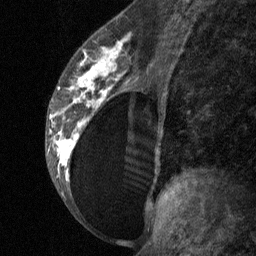
Breast MRI (dynamic contrast-enhanced), one sagittal slice; position 36 of 64 along the scan axis; dynamic contrast-enhanced study with each time point stored as its own series, time point 2 of 3 at this slice position (early post-contrast, ordered by acquisition time); 1.5 T; TE 4.8 ms, TR 27 ms; 2 mm slice thickness; 256 × 256 image matrix, field of view 180 × 180 mm. Patient: female, 34 years. Case-level facts recorded for this patient, not image findings: setting: breast cancer imaged before/during neoadjuvant chemotherapy; receptor status: HR-positive, HER2-negative.
Structures marked on this image (semi-automatically segmented with operator editing):
- analysis volume of interest (the breast-tissue region the enhancement analysis was run in; not a lesion): bounding box [x1, y1, x2, y2] px = [45, 23, 157, 197]
- tumour enhancement mask (voxels above the 90 % enhancement threshold inside the analysis volume of interest): [50, 39, 125, 181]